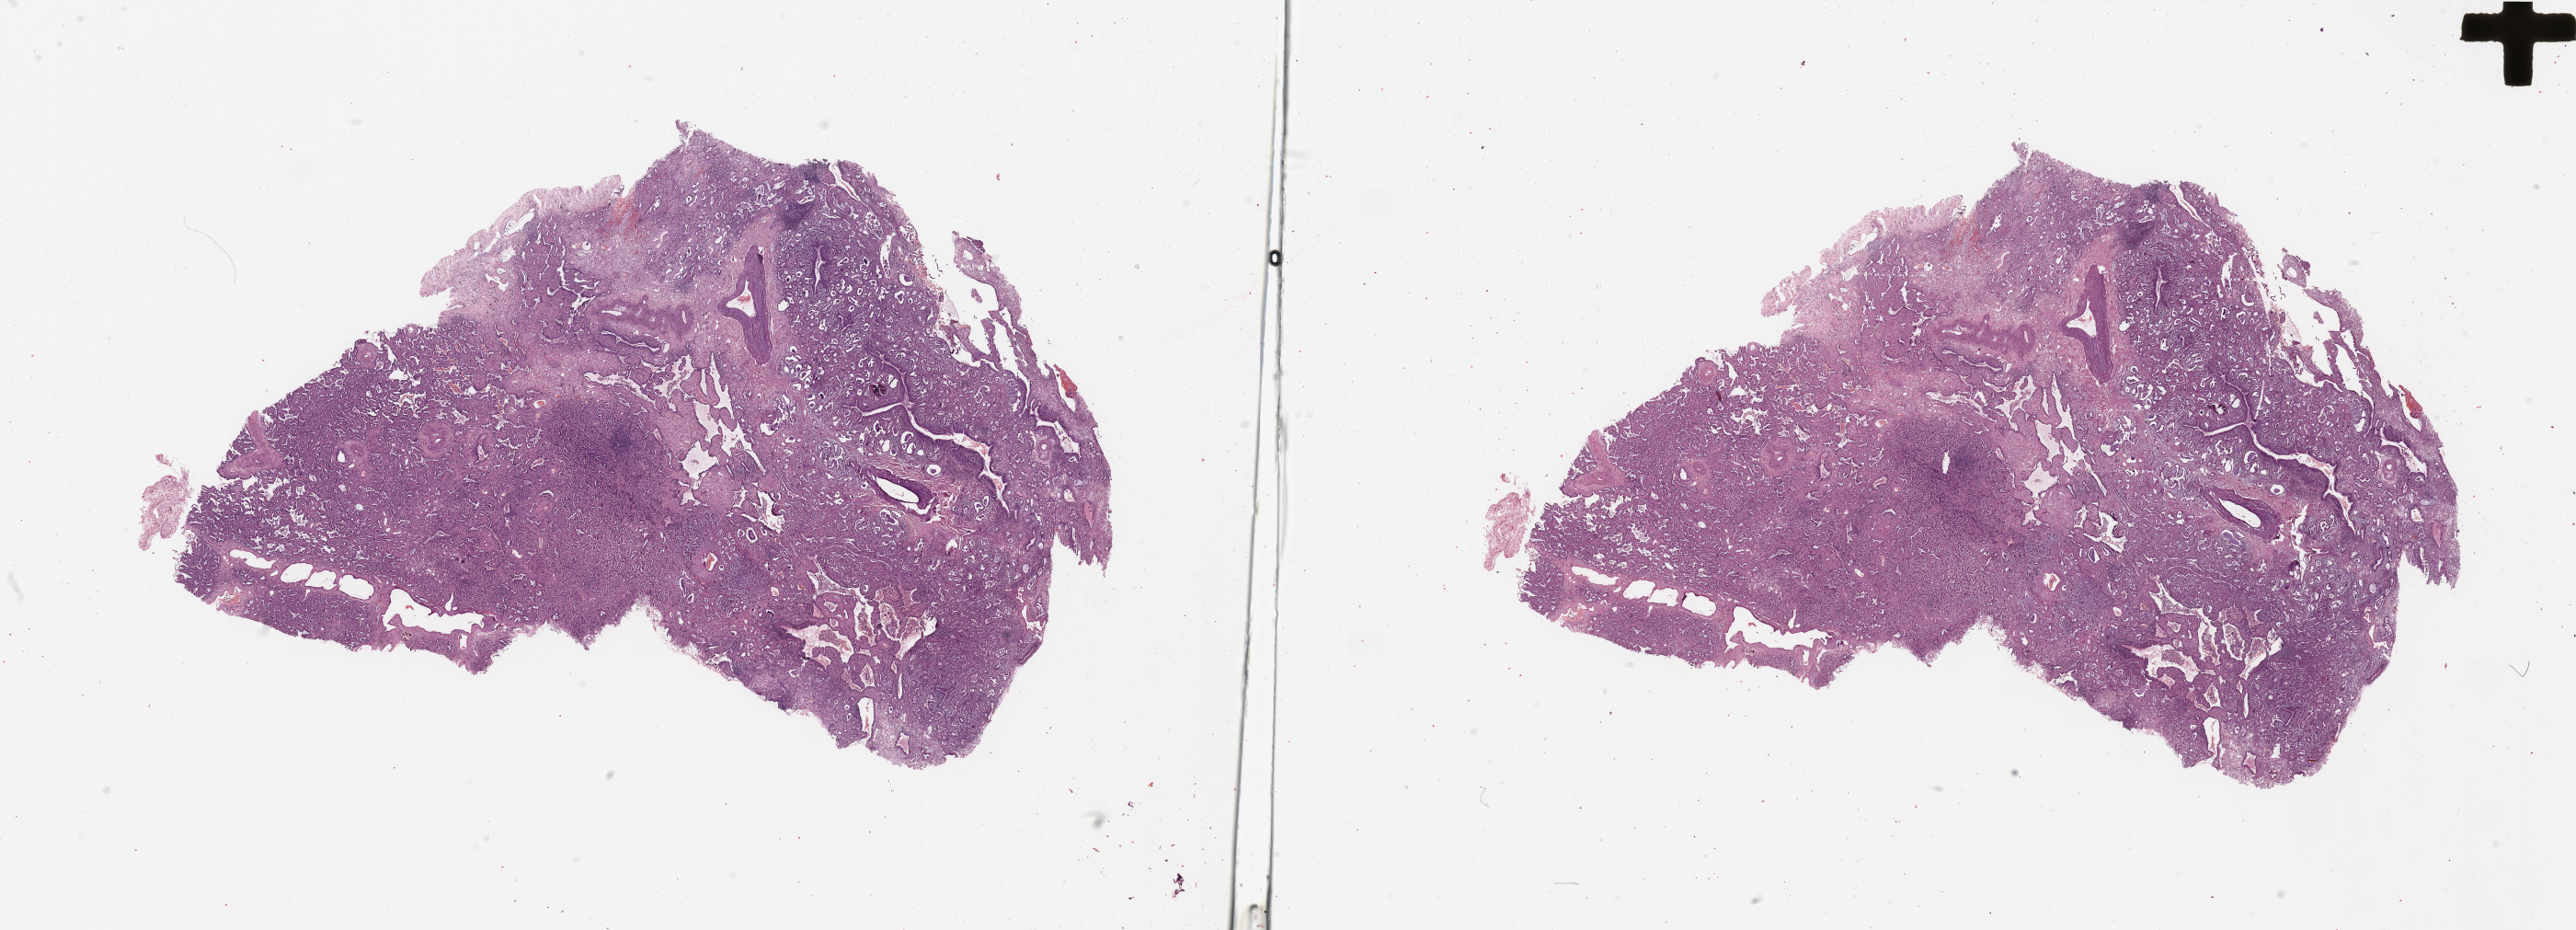
Whole-slide histology image, H&E-stained — low-resolution overview of the scanned area, about 44.3 x 16.0 mm; tumour tissue sample, lung. Patient: female, age 70 years.
Histologic diagnosis: Adenocarcinoma, NOS.